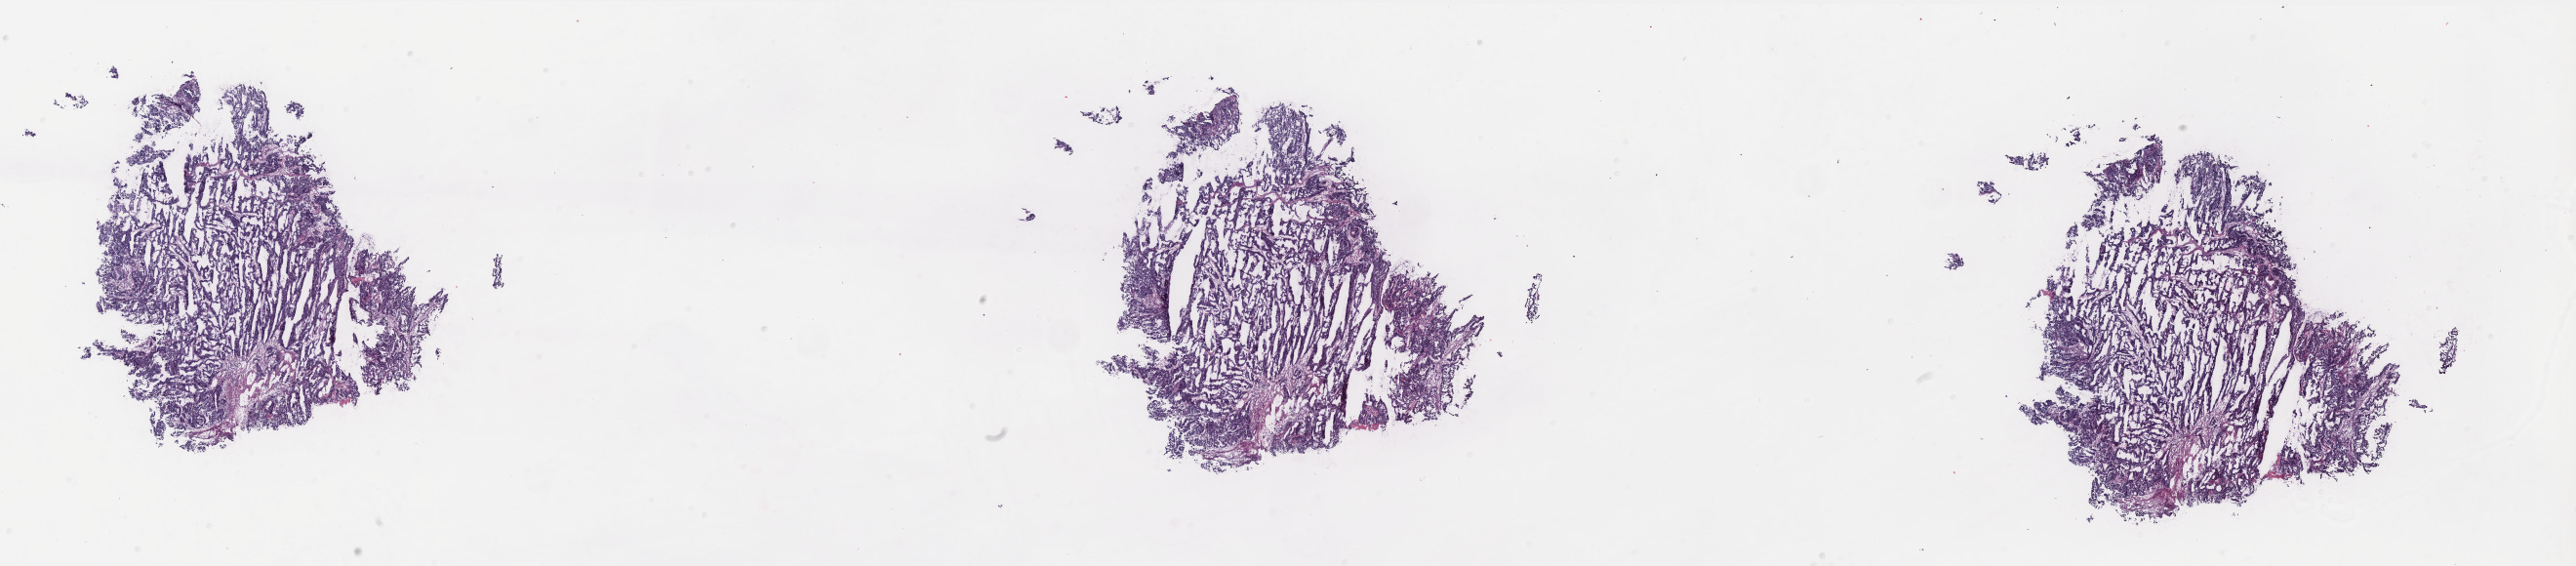
Whole-slide histology image, Hematoxylin and eosin (H&E) stained — low-resolution overview of the scanned area, about 42.3 x 9.3 mm. Frozen section. Sample: primary tumour, uterus. Patient: female, age at initial diagnosis 57 years. Histologic grade: G3 (poorly differentiated). Composition of this section per pathologist review: tumour cells 79%, tumour nuclei 85%, normal cells 0%, stromal cells 20%, necrosis 1%. Infiltration values recorded for this section: lymphocyte infiltration 5%, monocyte infiltration 1%, neutrophil infiltration 0%.
* lymph nodes positive (case pathology): 0 of 19 examined
* FIGO stage: IA
* histologic diagnosis: Endometrioid adenocarcinoma, NOS (endometrium)